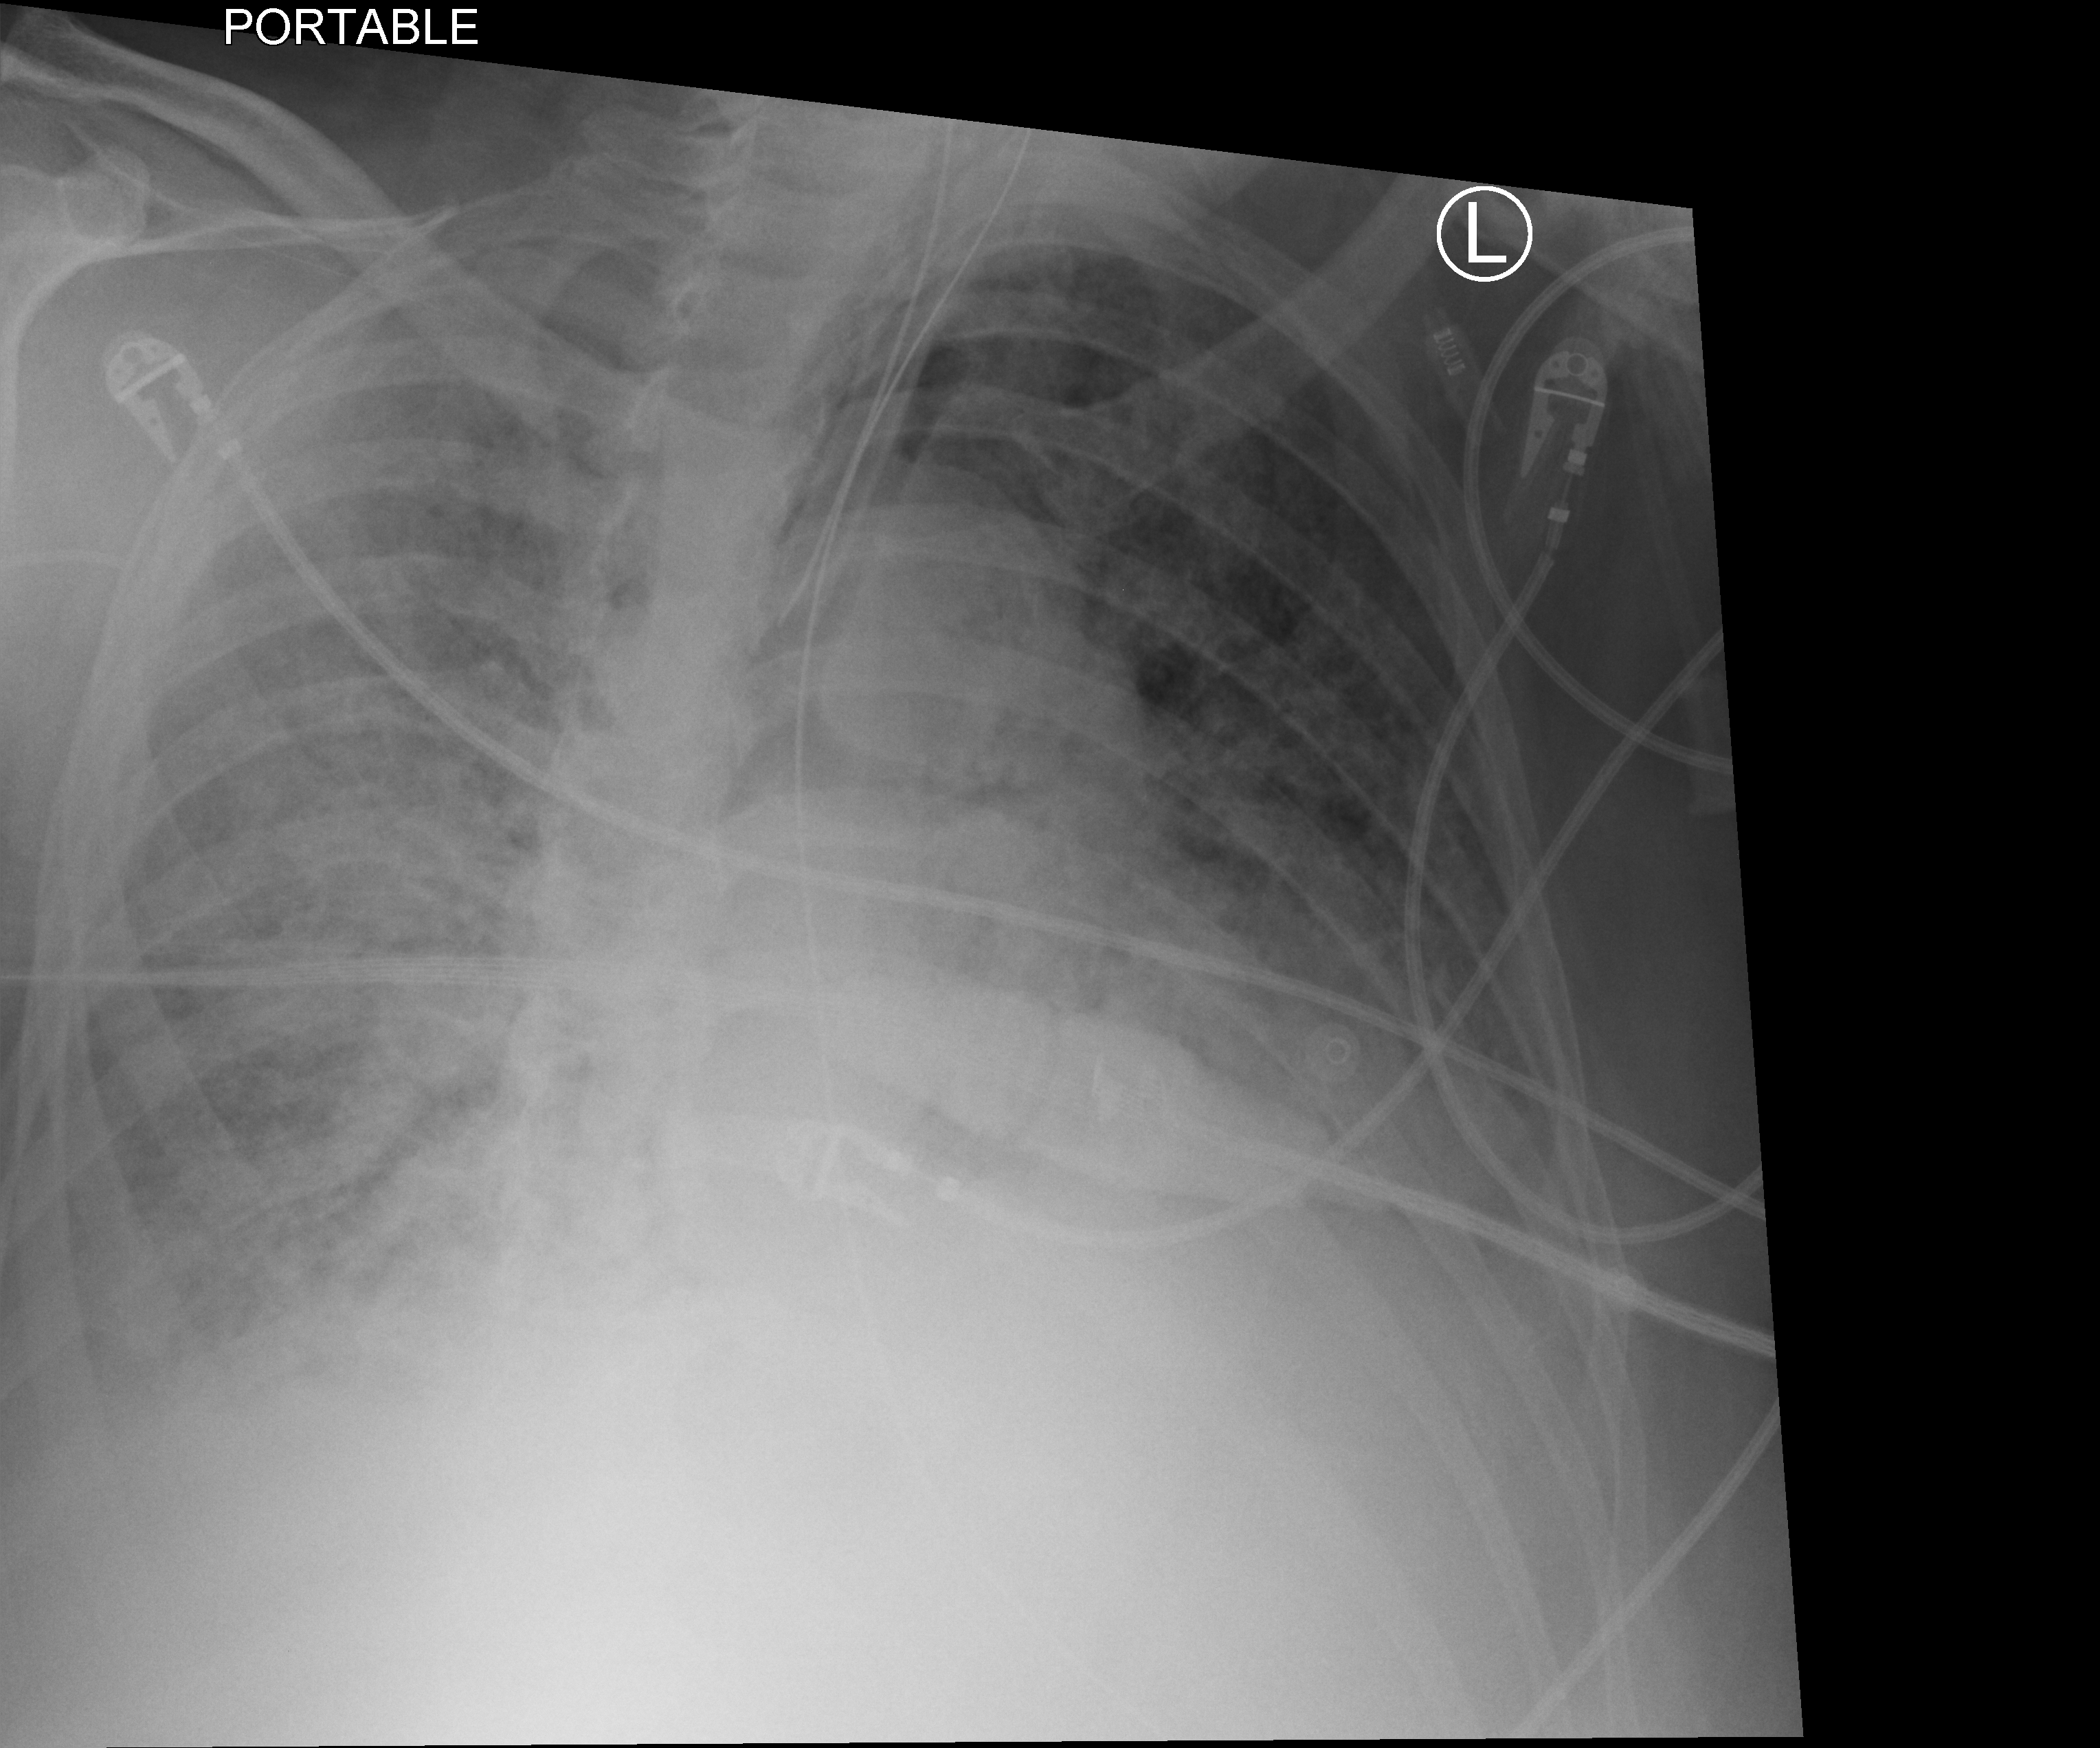
Bedside chest radiograph (computed radiography), anteroposterior (AP) projection. Male patient hospitalised with COVID-19, age 60–74 years.
From the hospital-stay record, not from the radiograph (when in the stay this image was taken is not recorded):
- mechanically ventilated during this hospital stay: yes
- admitted to intensive care during this hospital stay: yes